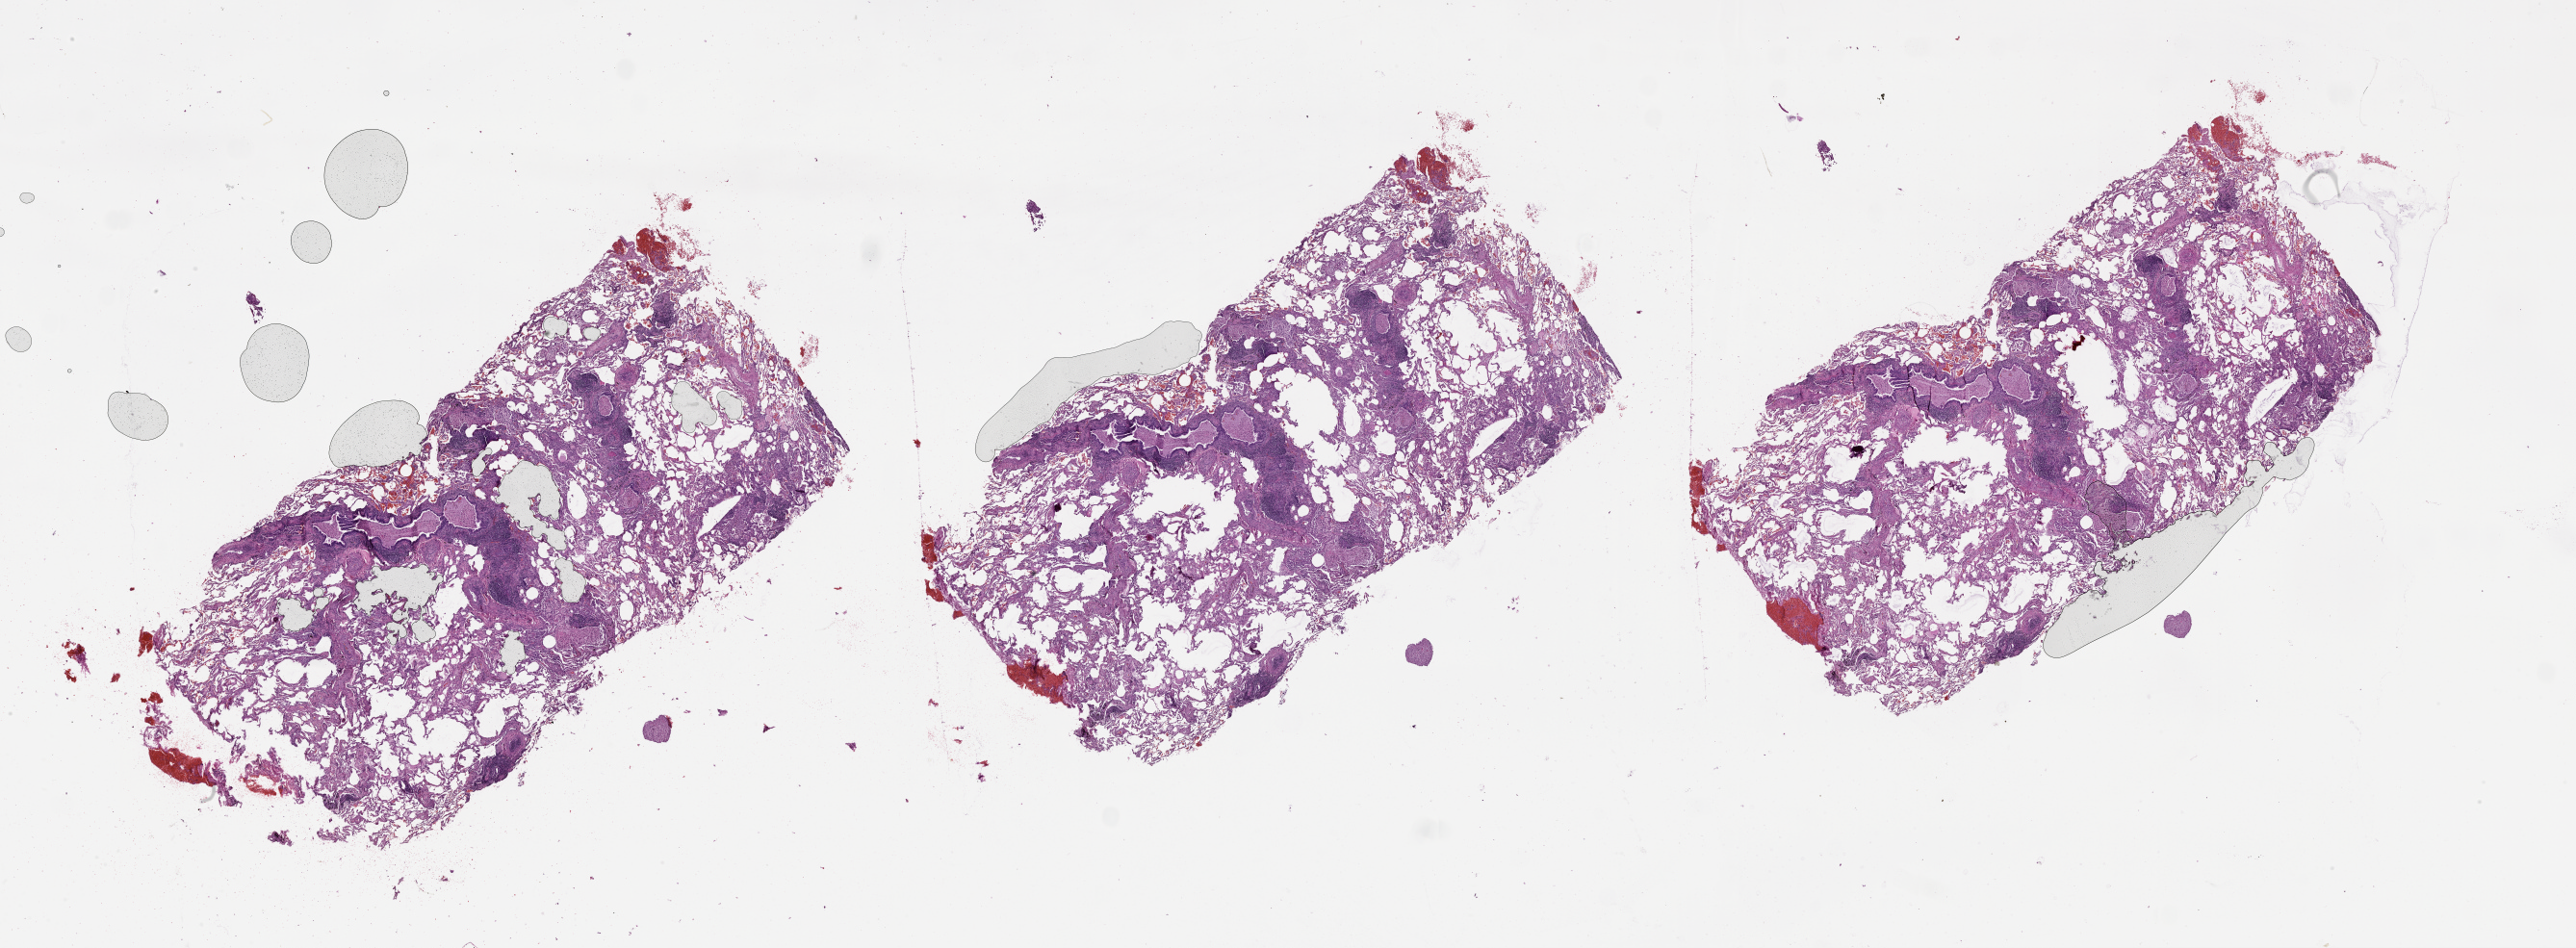
Whole-slide histology image, Hematoxylin and eosin (H&E) stained, a low-resolution overview of the entire scanned area, about 43.1 x 15.9 mm (from a 20x scan); normal (non-tumour) tissue sample, lung. 53-year-old male patient.
This section: normal (non-tumour) tissue from the same patient. Patient diagnosis (cohort enrolment): squamous cell carcinoma (lung).